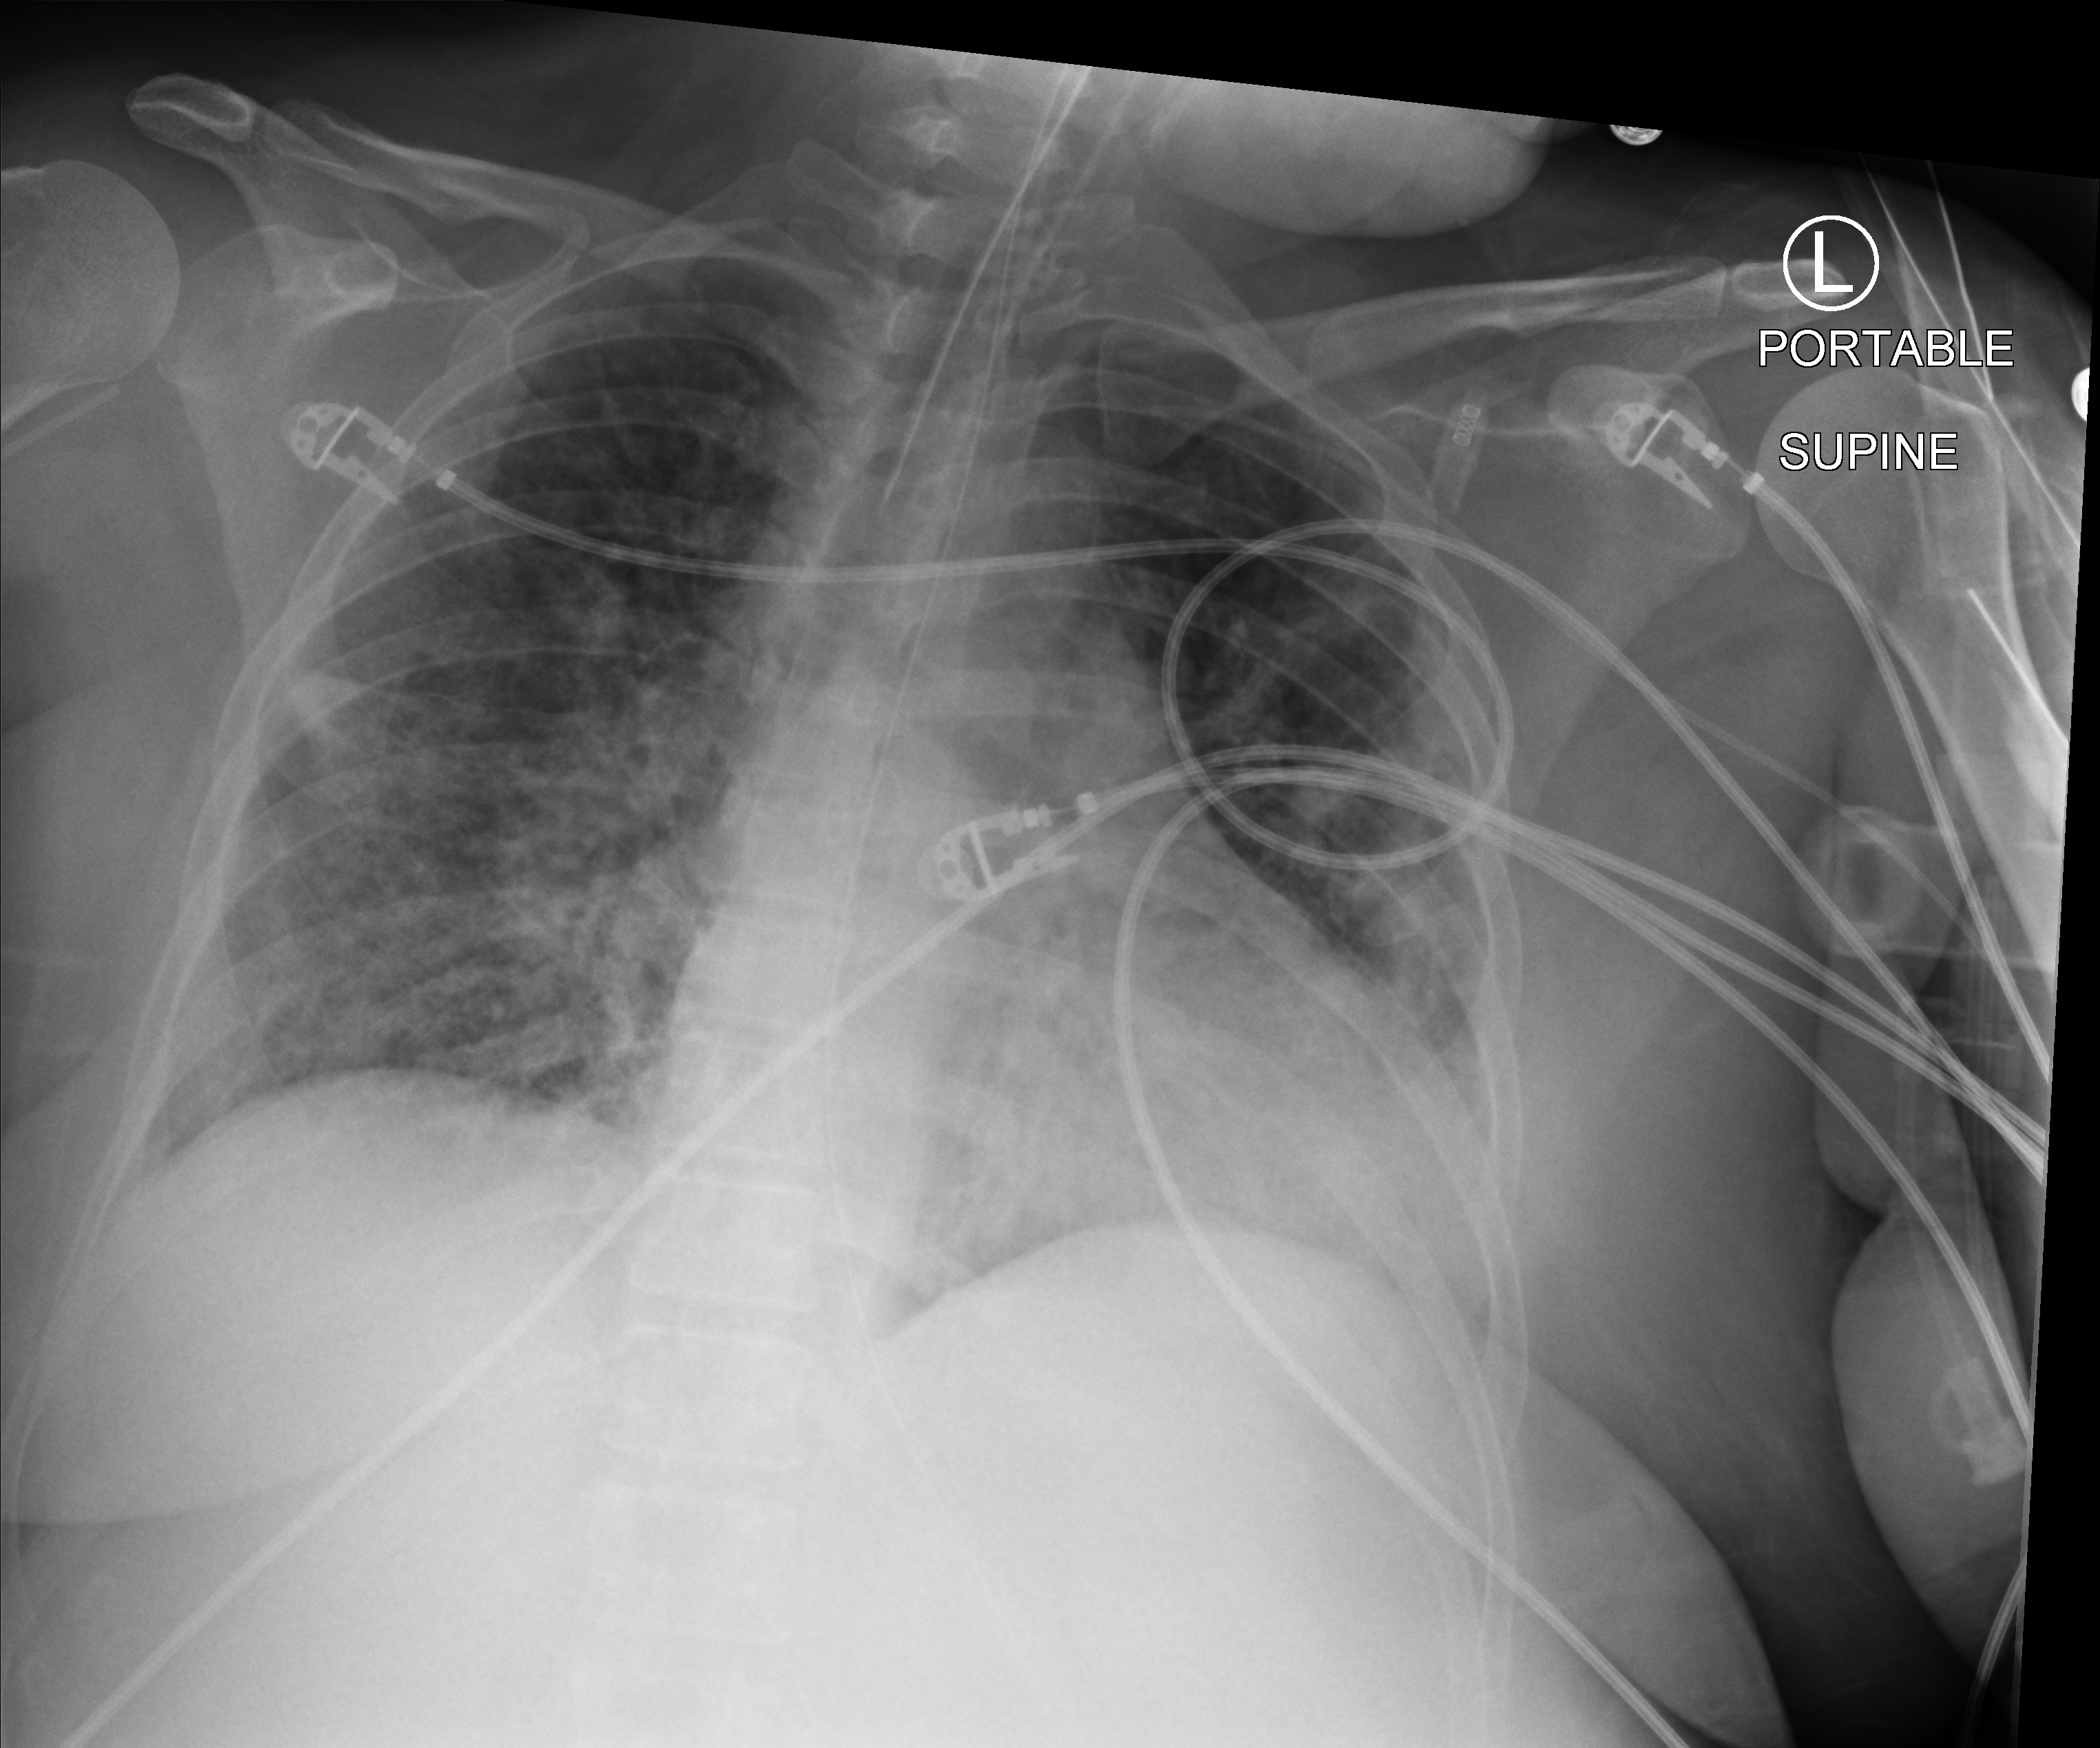
Chest X-ray (portable). Patient hospitalised with COVID-19; female, aged 18–59 years.
From the hospital-stay record, not from the radiograph (when in the stay this image was taken is not recorded):
- length of hospital stay: 31 days